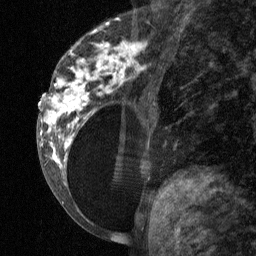
Breast MRI (dynamic contrast-enhanced), one sagittal slice. Dynamic contrast-enhanced study with each time point stored as its own series, time point 2 of 3 at this slice position (early post-contrast, ordered by acquisition time). 1.5 T. TE 4.8 ms, TR 27 ms. 256 × 256 image matrix. Patient: female, 34 years. From the clinical record (not read from this slice): setting: breast cancer imaged before/during neoadjuvant chemotherapy; receptor status: HR-positive, HER2-negative.
Structures marked on this image (semi-automatic segmentation, software-assisted and operator-edited):
- analysis volume of interest (the breast-tissue region the enhancement analysis was run in; not a lesion): bounding box (x1, y1, x2, y2) in pixels: (41, 23, 157, 197)
- tumour enhancement mask (voxels above the 90 % enhancement threshold inside the analysis volume of interest): (41, 30, 146, 174)